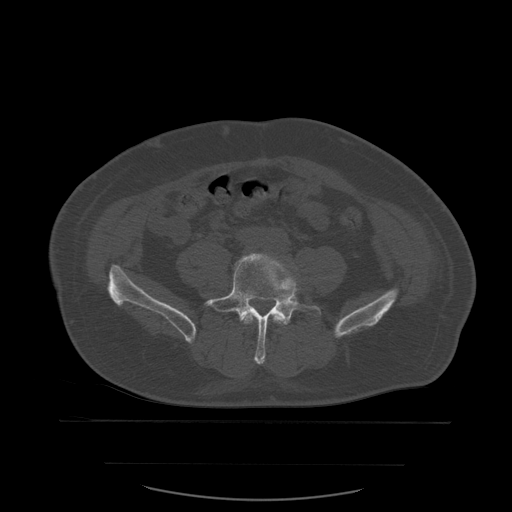
CT including the spine, one axial slice. Slice 144 of 590 in the series (ordered by position). Bone window (W 1800 / L 400 HU). 1.25 mm slice thickness. 512 × 512 image matrix. Patient age 71 years. From the clinical record (not read from this slice): primary cancer: lung; vertebrae with lytic lesions (as recorded): T1, T2, L5, S1.
Outlined on this slice (semi-automatically segmented with operator editing):
- L4 vertebra: bounding box <243,314,281,324> (left, top, right, bottom; pixels)
- L5 vertebra: <204,253,322,365>